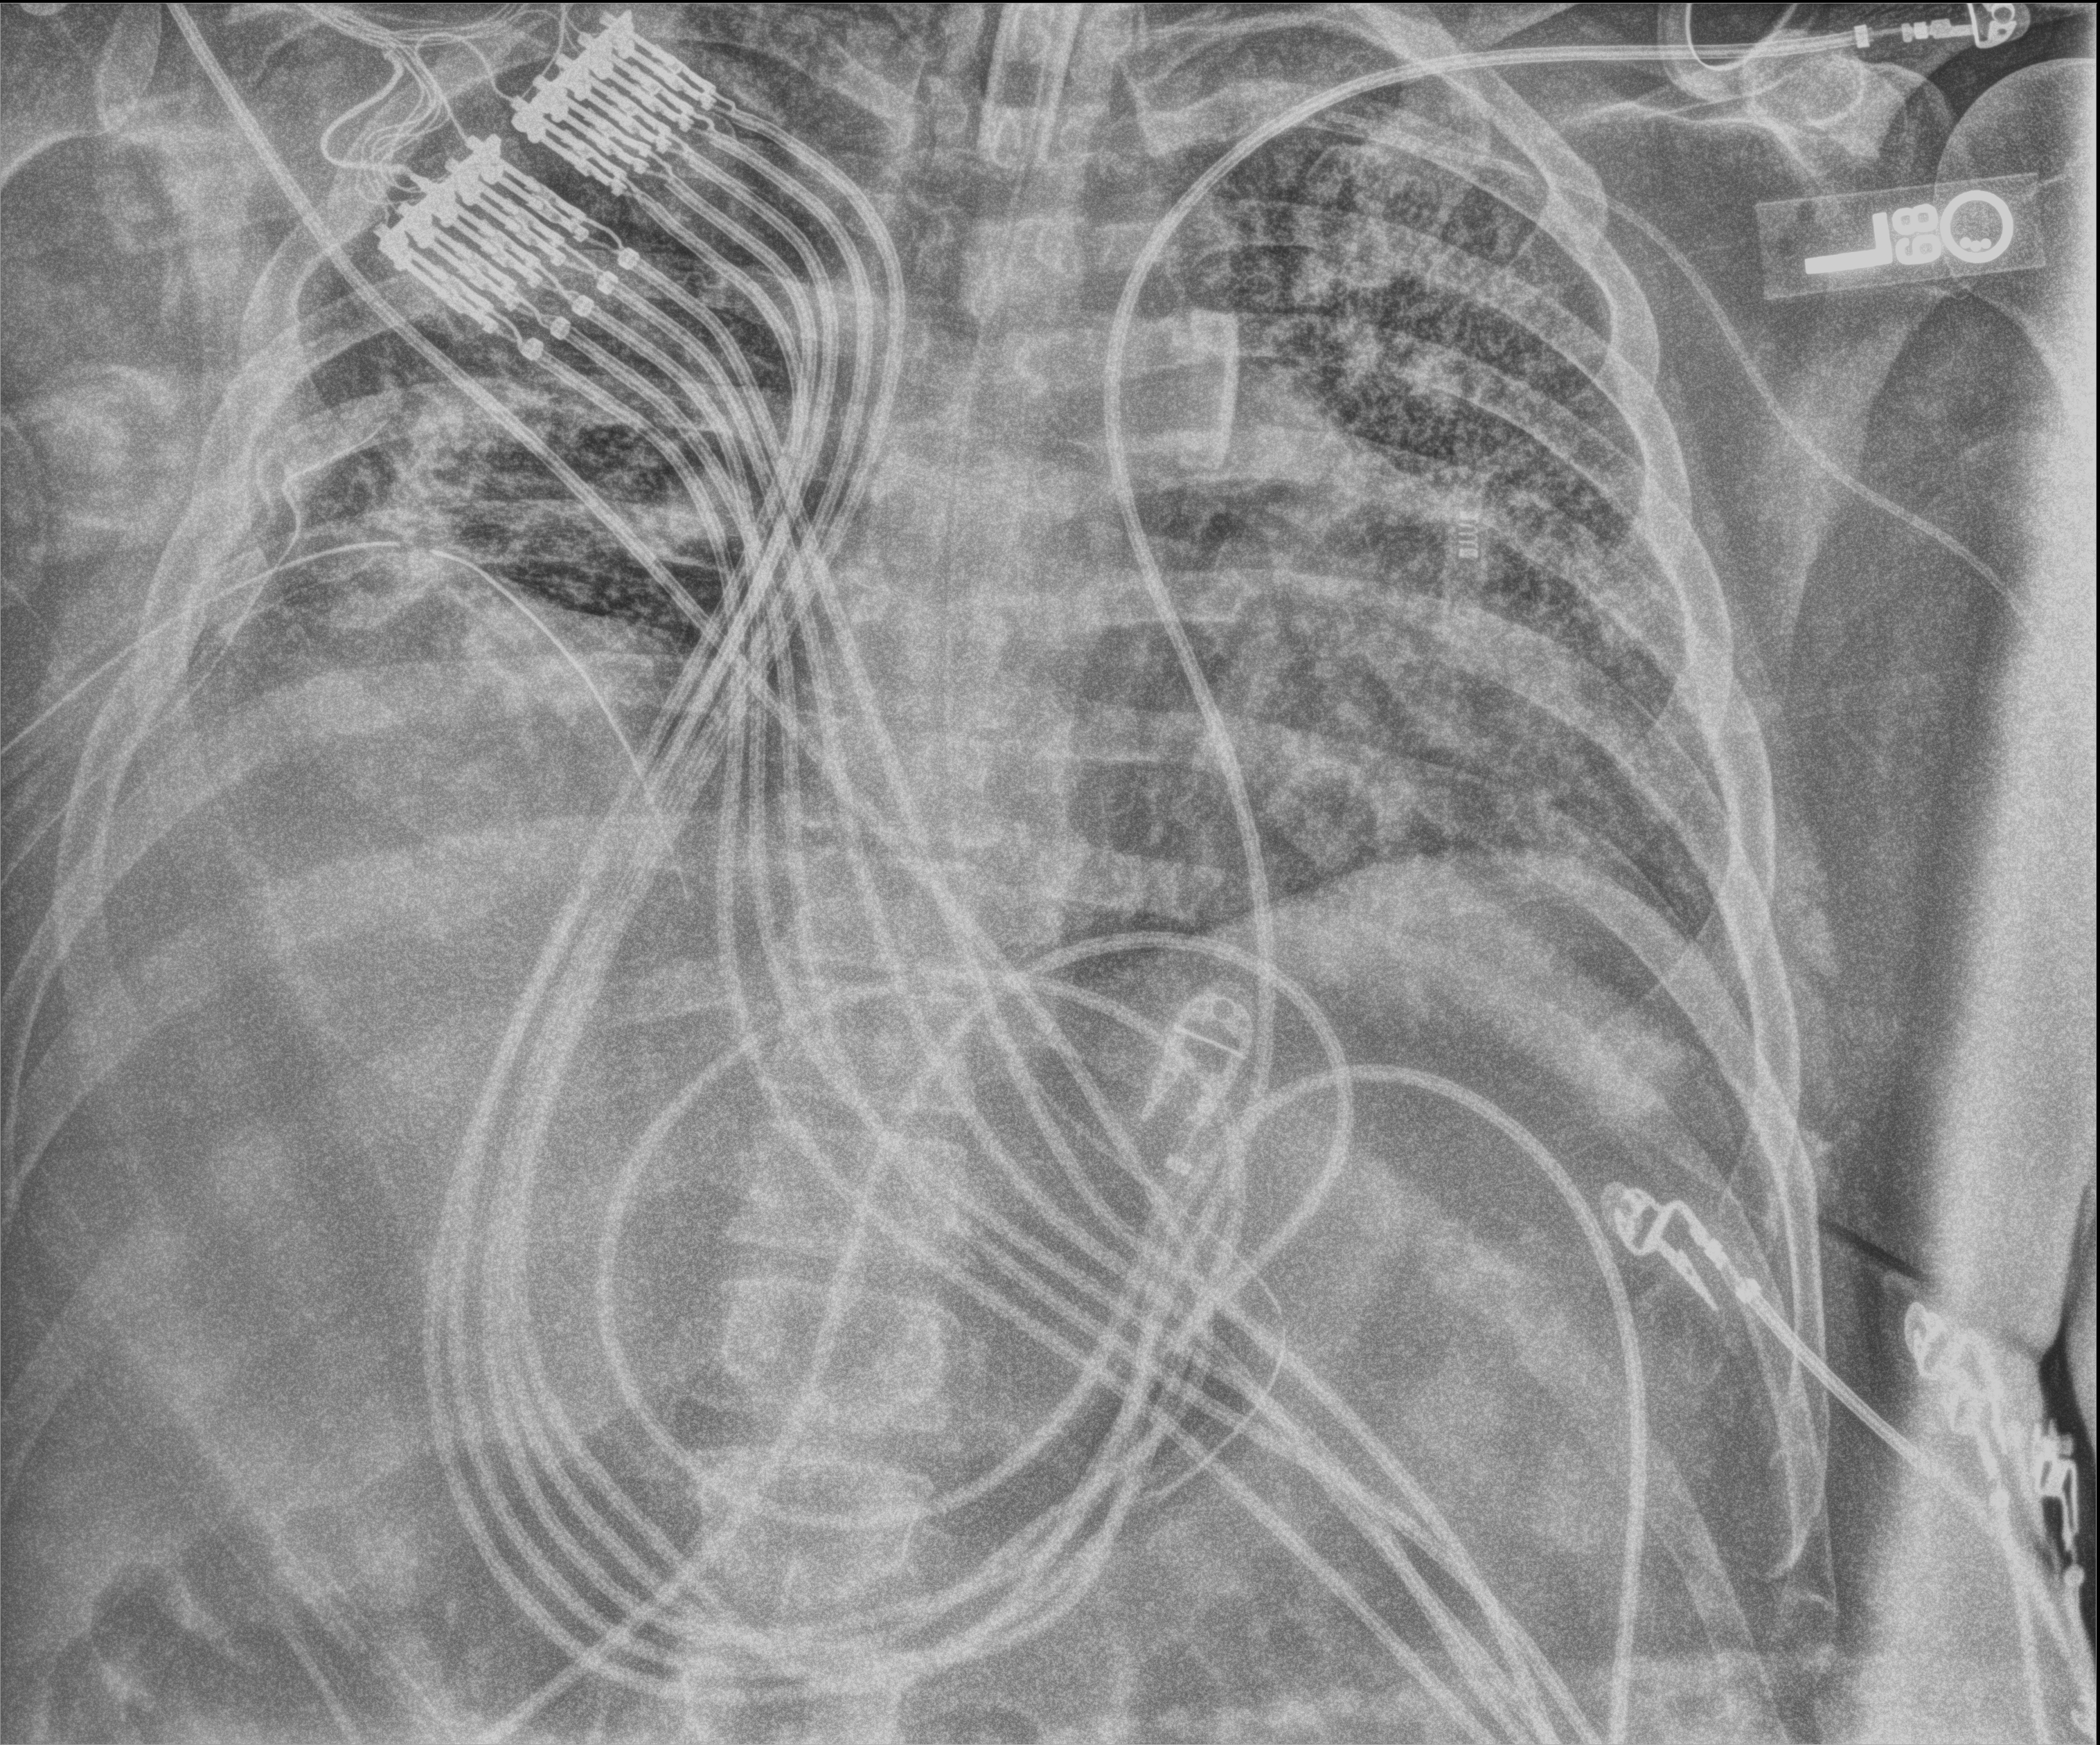
Chest radiograph (digital radiography); anteroposterior (AP) projection. Male patient hospitalised with COVID-19, age 18–59 years.
From the hospital-stay record, not from the radiograph (when in the stay this image was taken is not recorded):
- smoking status (admission record): never
- diabetes (admission record): no